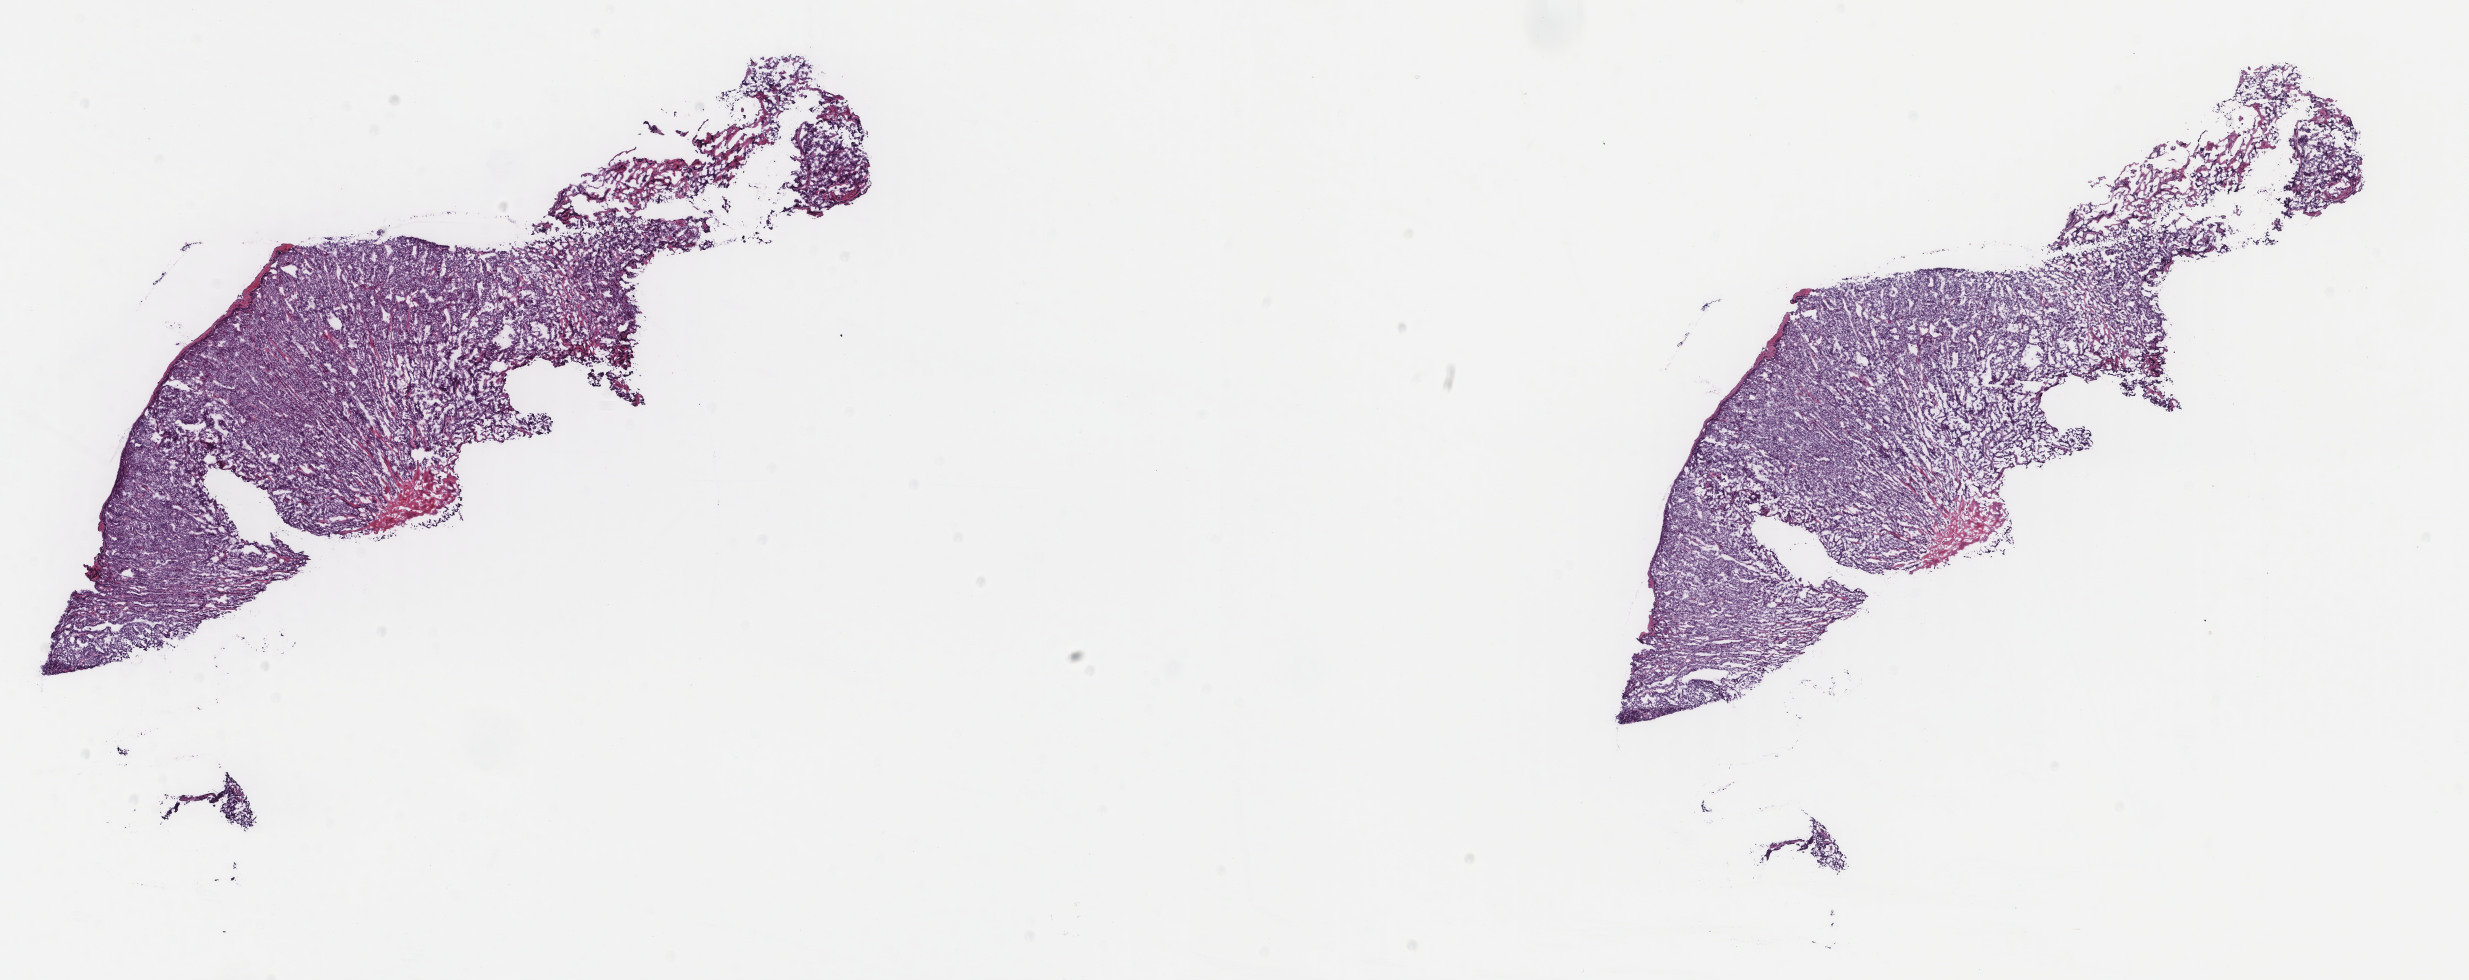
H&E whole-slide image — low-resolution overview of the scanned area, about 19.6 x 7.8 mm (from a 40x scan), frozen section from the top of the tissue portion, sample: primary tumour, thyroid. Male, age 82 years at initial diagnosis. Slide review estimates, as recorded: tumour cells 100%, tumour nuclei 95%, normal cells 0%, stromal cells 0%, necrosis 0%. Infiltration values recorded for this section: lymphocyte infiltration 0%, monocyte infiltration 0%, neutrophil infiltration 0%.
* lymph nodes positive (case pathology): 0 of 2 examined
* laterality: right
* diagnosis: Papillary adenocarcinoma, NOS (thyroid gland)
* AJCC pathologic stage: III (6th edition)